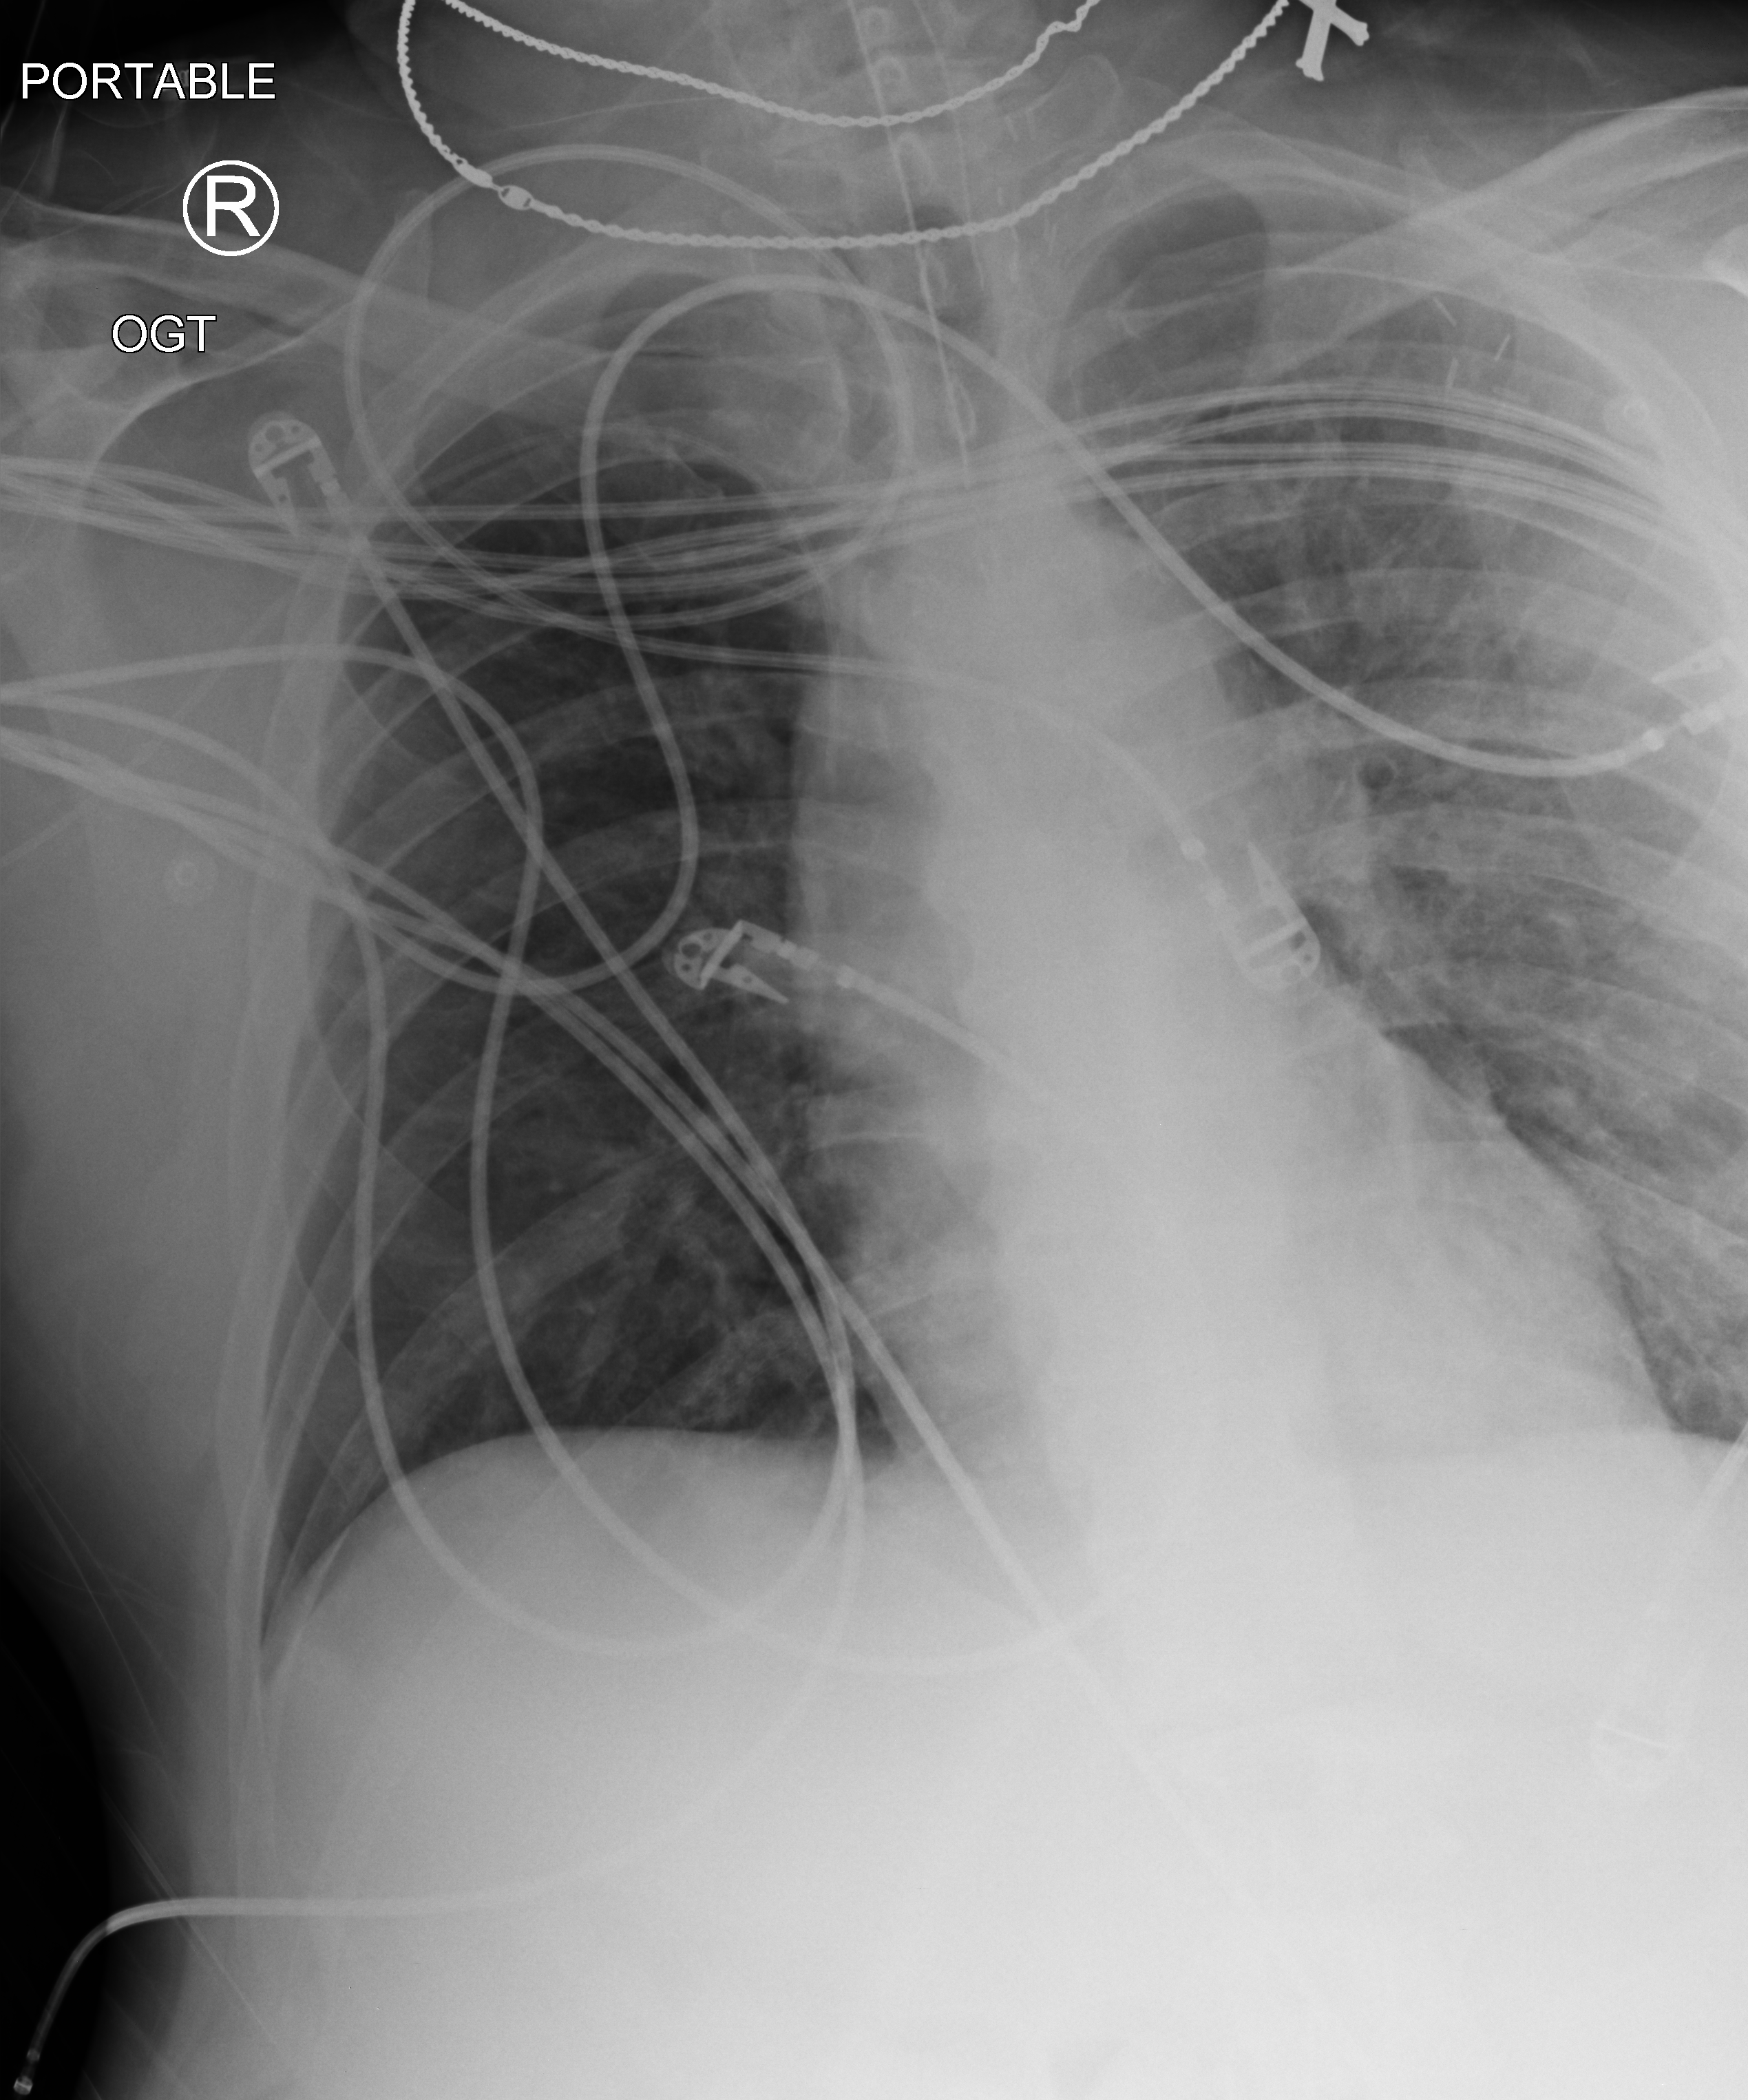
Bedside chest radiograph (computed radiography), anteroposterior (AP) projection. Patient hospitalised with COVID-19, aged 18–59 years.
Admission-level facts for this patient (not findings on this image; timing relative to this image not recorded):
- admitted to intensive care during this hospital stay: yes
- length of hospital stay: 19 days